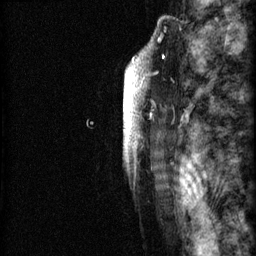
Breast MRI (dynamic contrast-enhanced), one sagittal slice; position 57 of 60 along the scan axis; 3 images stored at this slice position (order not interpretable as contrast timing); 1.5 T; TE 4.2 ms, TR 22.7 ms; 2 mm slice thickness; 256 × 256 image matrix. Patient: female, 48 years. Case-level facts recorded for this patient, not image findings: setting: breast cancer imaged before/during neoadjuvant chemotherapy; receptor status: triple-negative.
Annotated regions visible in this slice (semi-automatic segmentation, software-assisted and operator-edited):
- analysis volume of interest (the breast-tissue region the enhancement analysis was run in; not a lesion): bounding box [x1, y1, x2, y2] px = [86, 30, 173, 207]
- tumour enhancement mask (voxels above the 90 % enhancement threshold inside the analysis volume of interest): [123, 44, 164, 169]